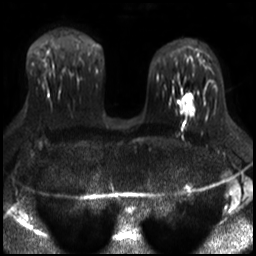
Breast MRI, one axial slice; position 18 of 30 along the scan axis; diffusion-weighted series; image 2 of 4 stored at this slice position (different b-values; order by instance number); 3 T; 4 mm slice thickness; 256 × 256 image matrix. Female patient.
Annotated regions visible in this slice (outlined manually by an expert reader):
- tumour on diffusion-weighted imaging: bounding box <182,100,185,106> (left, top, right, bottom; pixels)